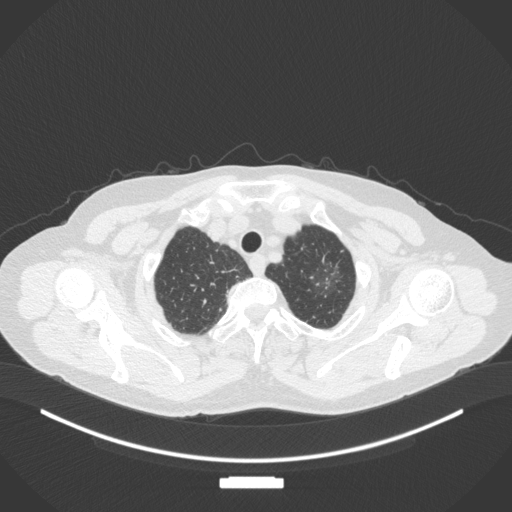
Chest CT, one axial slice. Lung window (W 1500 / L -600 HU). 1 mm slice thickness. 512 × 512 image matrix, field of view 400 × 400 mm. Female patient, age 64 years. Case-level facts recorded for this patient, not image findings: clinical TNM (as recorded): T1c N0 M0; histopathological grade: G1.
Annotated regions visible in this slice (bounding box drawn by a radiologist):
- lung tumour (recorded histology: adenocarcinoma): bounding box <316,260,342,289> (left, top, right, bottom; pixels)